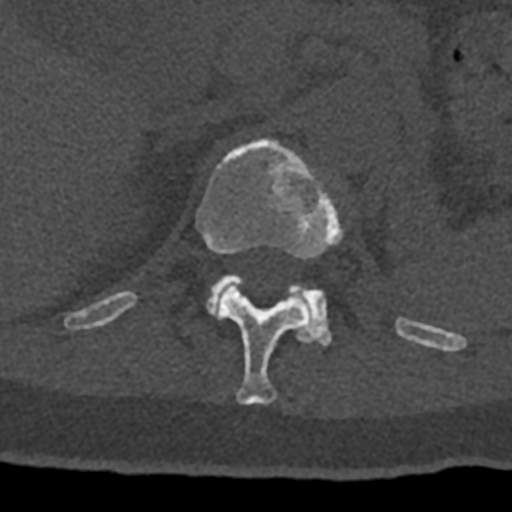
CT including the spine, one axial slice. Position 476 of 797 along the scan axis. Reconstruction kernel Br40s/3. 120 kVp. Bone window (W 1800 / L 400 HU). 0.5 mm slice thickness. 512 × 512 image matrix. Patient: male, 74 years. From the clinical record (not read from this slice): primary cancer: renal; vertebrae with lytic lesions (as recorded): T10, L1, L2, L3, L4, L5.
Structures marked on this image (semi-automatic segmentation, software-assisted and operator-edited):
- L1 vertebra: bounding box (x1, y1, x2, y2) in pixels: (206, 274, 332, 346)
- T12 vertebra: (70, 139, 432, 405)